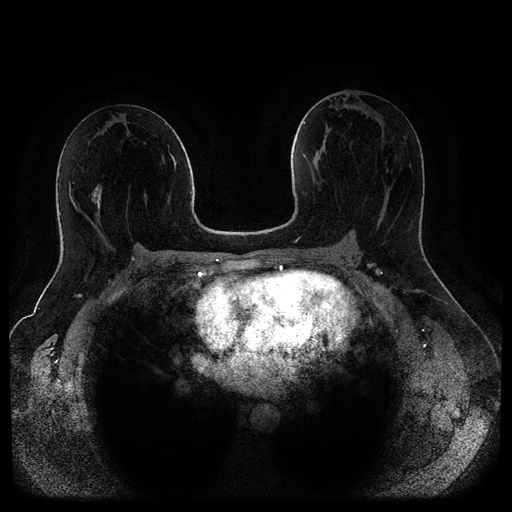
Breast MRI (dynamic contrast-enhanced, multi-phase), one axial slice. Position 51 of 116 along the scan axis. Dynamic contrast-enhanced series, time point 2 of 5 at this slice position (early post-contrast). 1.5 T. TE 2.6 ms, TR 5.3 ms. 2 mm slice thickness. 512 × 512 image matrix, field of view 370 × 370 mm. Female patient, age 44 years.
Annotated regions visible in this slice (semi-automatic segmentation, software-assisted and operator-edited):
- breast lesion (labelled benign in the annotation): bounding box [x1, y1, x2, y2] px = [92, 185, 101, 211]